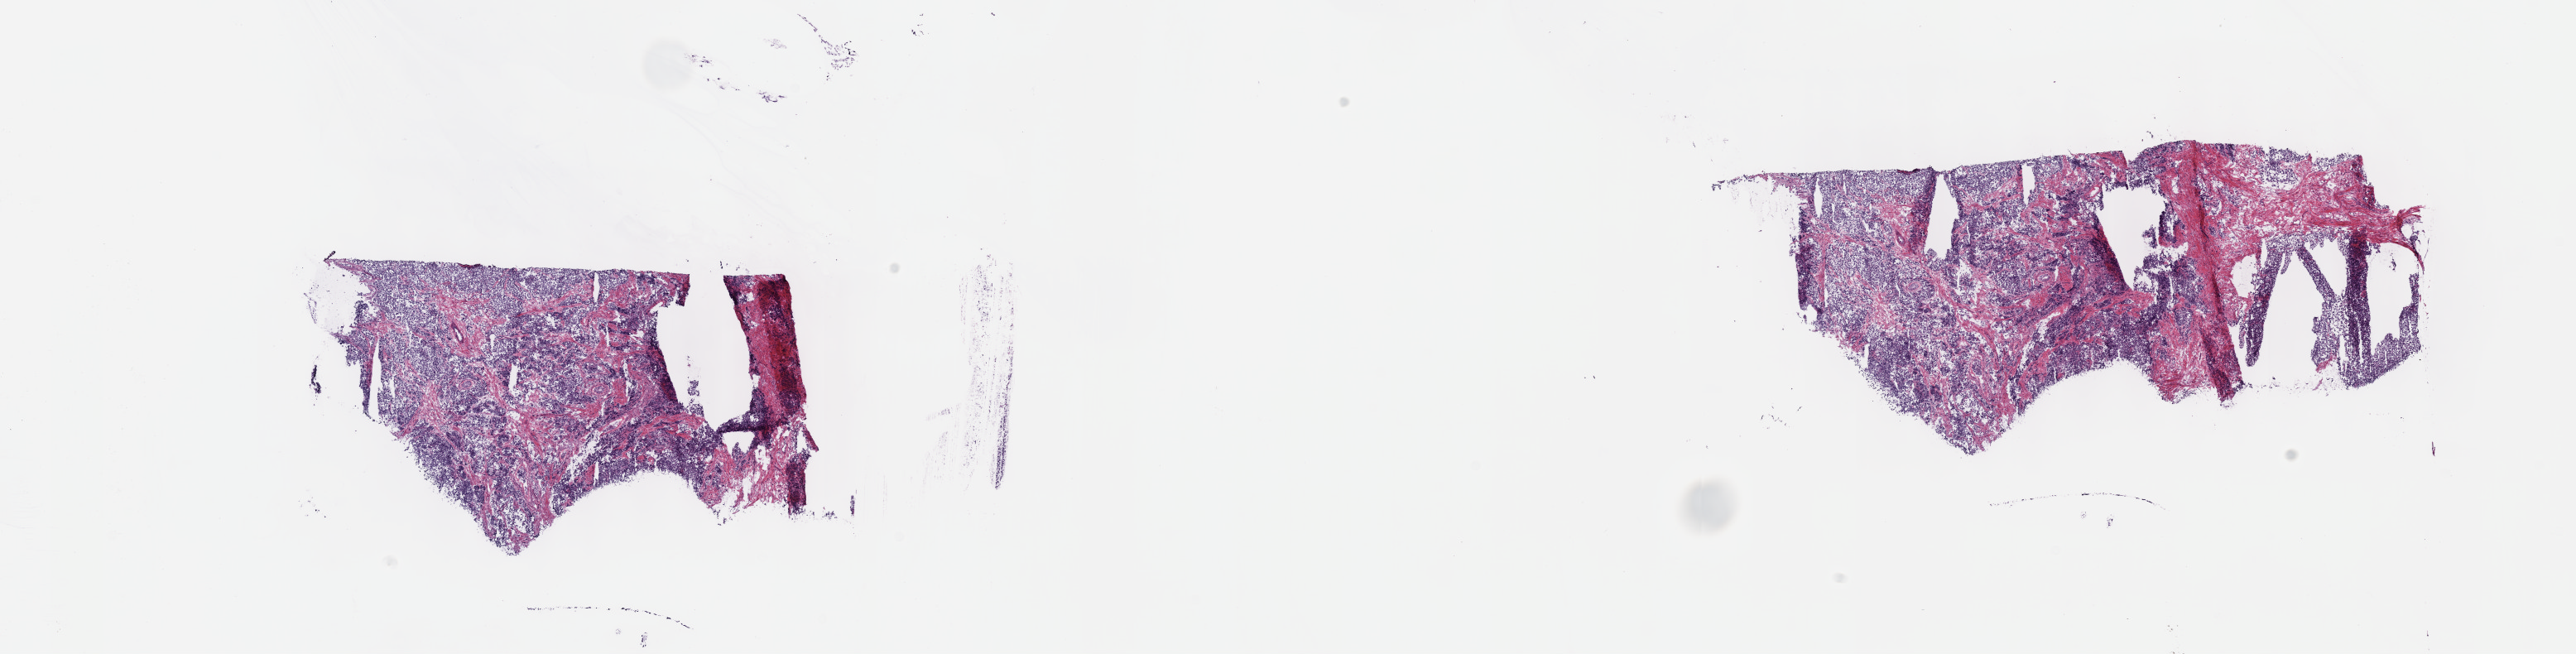
Hematoxylin and eosin (H&E) stained whole-slide image — whole scanned area (about 25.2 x 6.4 mm) shown as a low-resolution overview; frozen section; testis, primary tumour sample. Male, age 27 years at initial diagnosis. Slide review estimates, as recorded: tumour cells 60%, tumour nuclei 60%, normal cells 0%, stromal cells 30%, necrosis 10%. Inflammatory infiltration, as recorded: lymphocyte infiltration 70%, monocyte infiltration 25%, neutrophil infiltration 5%.
- AJCC pathologic stage: IB
- pathologic diagnosis: Seminoma, NOS